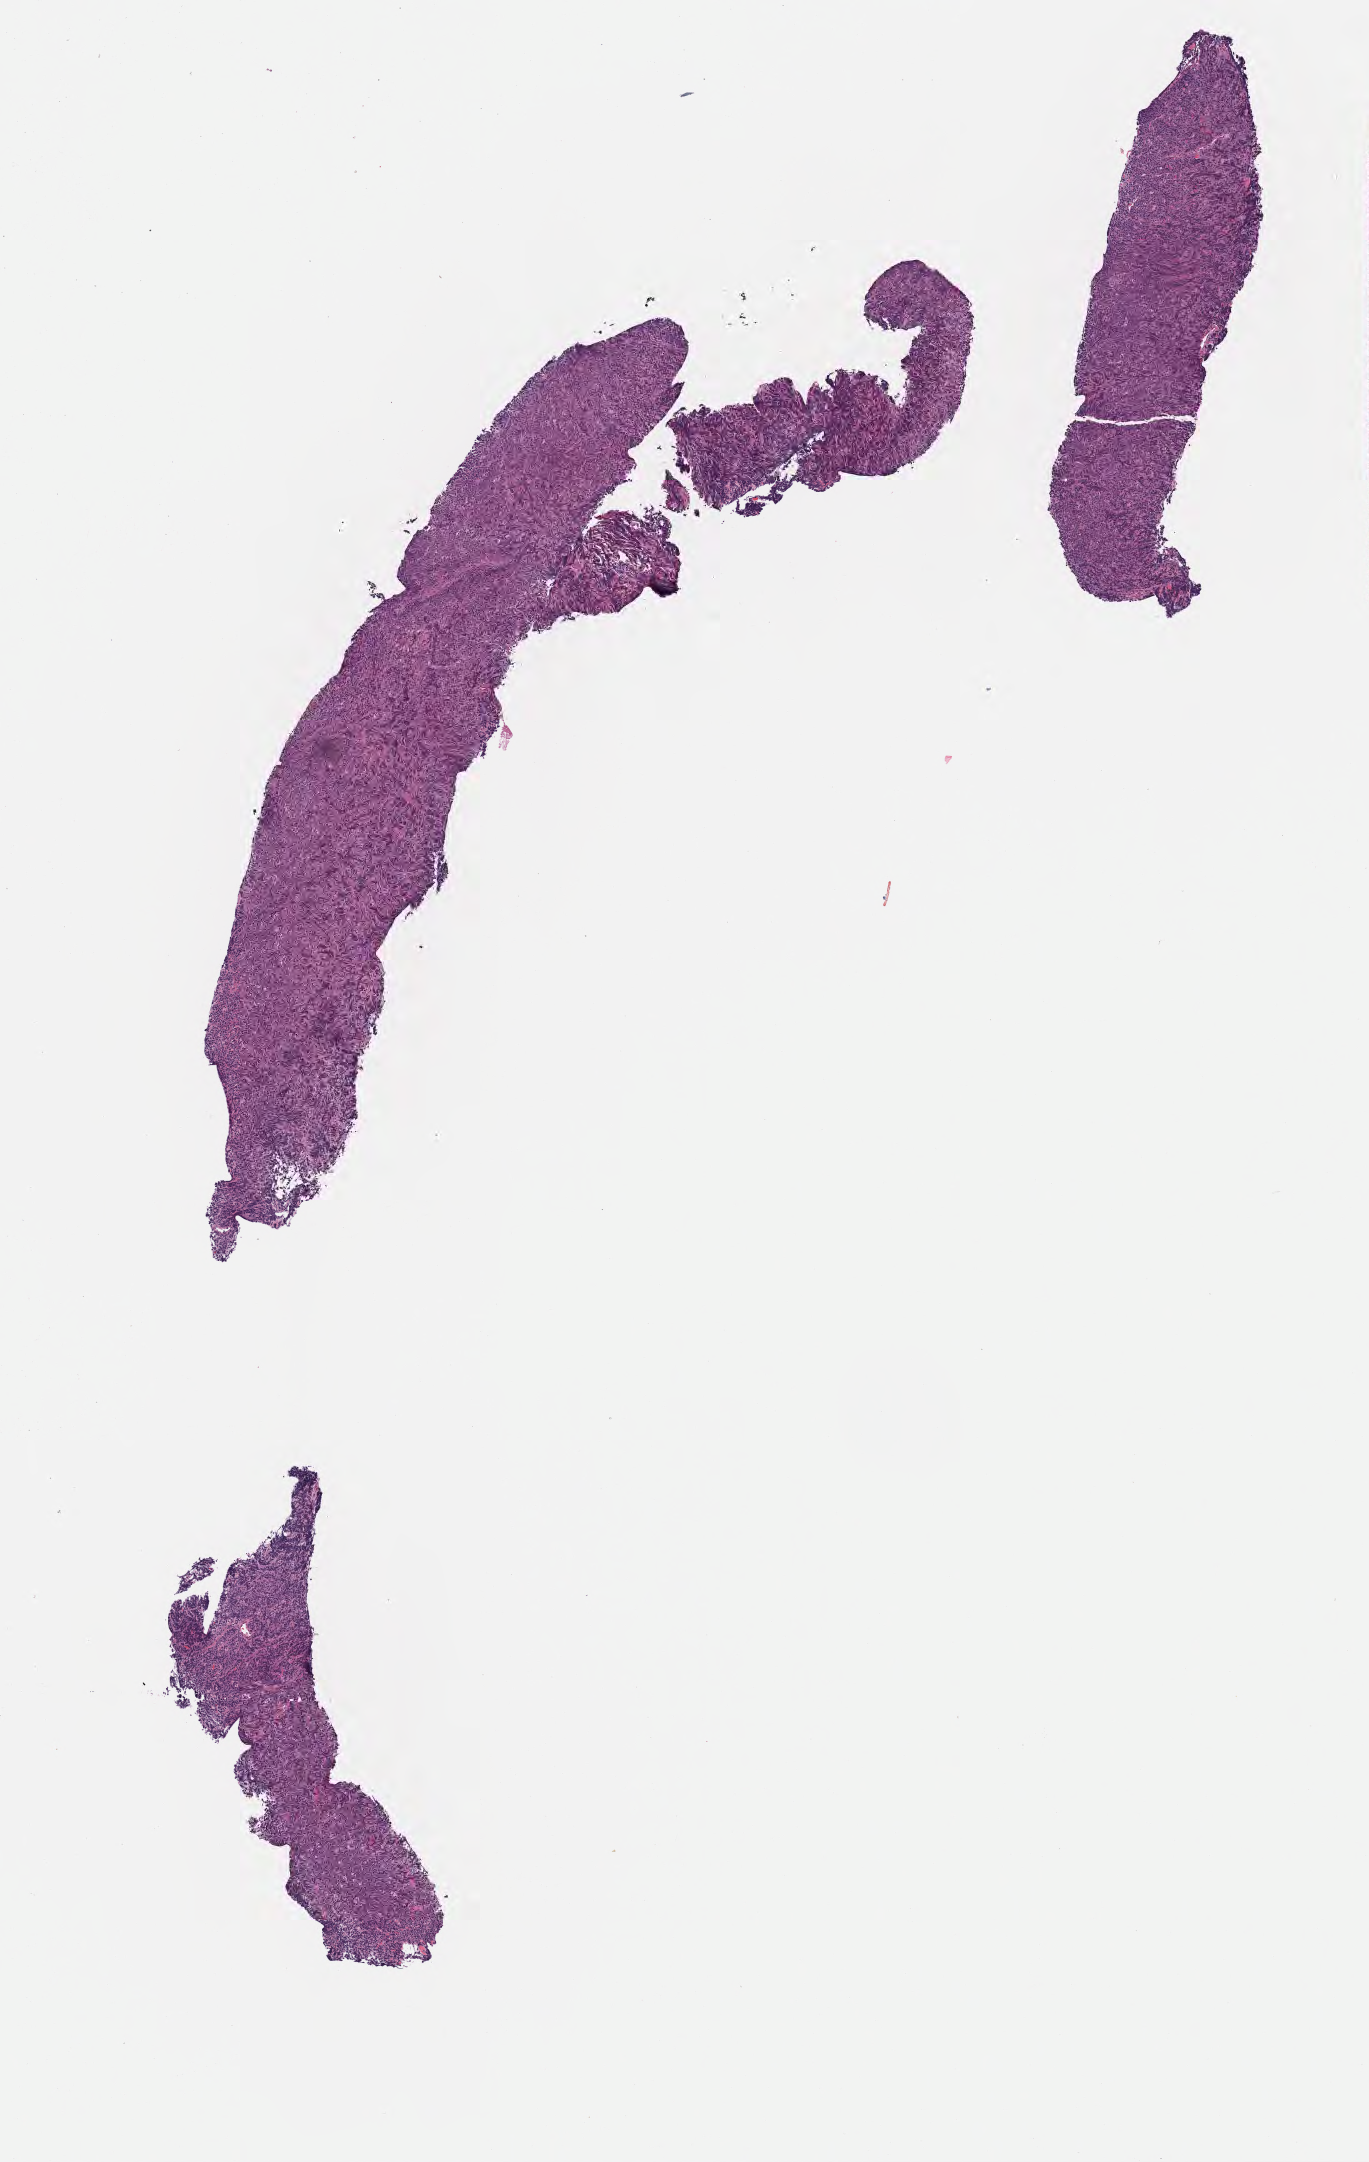
Hematoxylin and eosin (H&E) whole-slide image, whole scanned area (about 5.5 x 8.7 mm) shown as a low-resolution overview, tumor tissue. Male patient, 10 years old.
Histologic diagnosis: Diffuse large B-cell lymphoma, NOS.